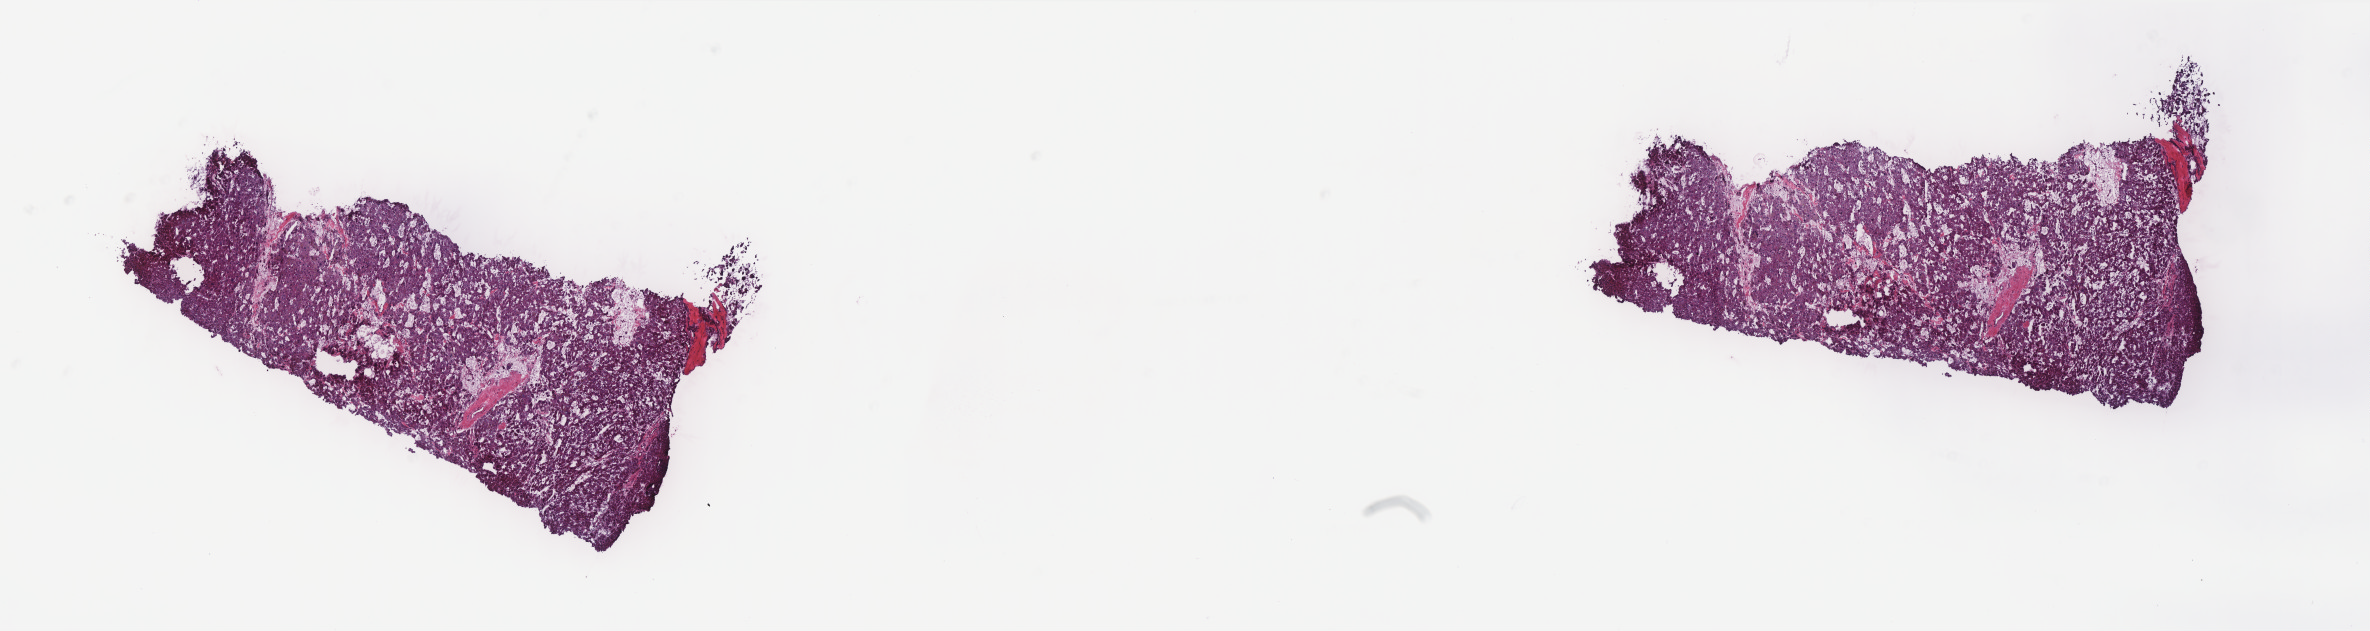
Digitized Hematoxylin and eosin (H&E) stained tissue section (whole slide) — a low-resolution overview of the entire scanned area, about 19.0 x 5.1 mm (acquisition: 40x scan), frozen section from the top of the tissue portion, sample: primary tumour, liver. Male, age 68 years at initial diagnosis. Histologic grade: G1 (well differentiated). Pathologist review of this section (percent, as recorded): tumour cells 100%, tumour nuclei 92%, normal cells 0%, stromal cells 0%, necrosis 0%. Infiltration values recorded for this section: lymphocyte infiltration 0%, monocyte infiltration 0%, neutrophil infiltration 0%.
• histologic diagnosis: Hepatocellular carcinoma, NOS
• AJCC pathologic stage: I (6th edition)